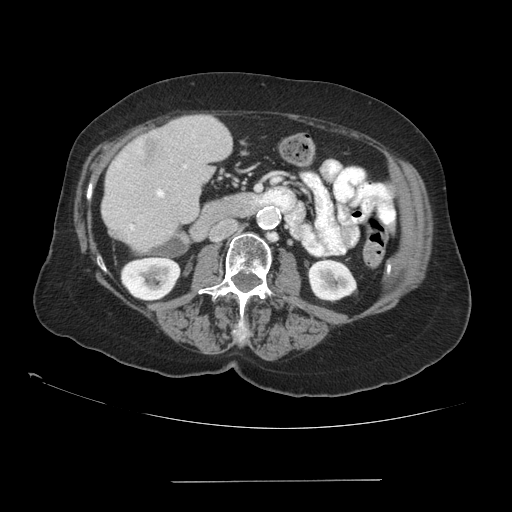
Contrast-enhanced abdominal CT (liver protocol), one axial slice; position 30 of 89 along the scan axis; 140 kVp; soft-tissue window (W 400 / L 40 HU); 2.5 mm slice thickness; 512 × 512 image matrix. Case-level facts recorded for this patient, not image findings: diagnosis: hepatocellular carcinoma (patient treated with transarterial chemoembolisation; whether this scan precedes or follows treatment is not stated here); TNM stage (as recorded): Stage-IVA; Child-Pugh class: A; tumour differentiation: poorly differentiated.
Outlined on this slice (semi-automatically segmented with operator editing):
- liver parenchyma outside the tumour (the mass and vessels are separate outlines, so this box may not span the whole liver): bounding box [x1, y1, x2, y2] px = [102, 116, 232, 250]
- mass: [134, 130, 164, 166]
- liver vessels: [130, 165, 186, 229]